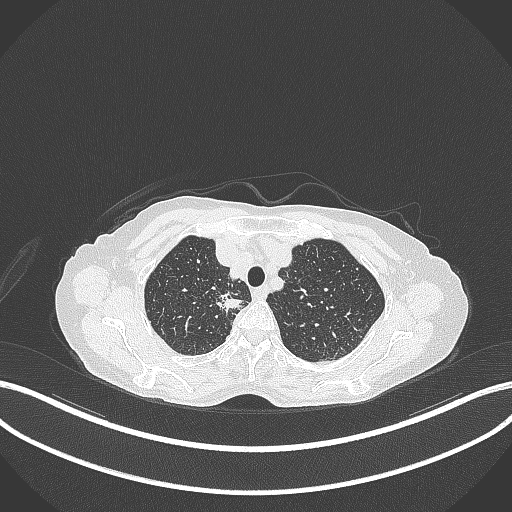
Chest CT, one axial slice; position 308 of 403 along the scan axis; reconstruction kernel B70f; 120 kVp; lung window (W 1500 / L -600 HU); 1 mm slice thickness; 512 × 512 image matrix. Female patient, age 75 years. From the clinical record (not read from this slice): clinical TNM (as recorded): T1c N1 M1.
Structures marked on this image (rectangle marked by the reading radiologist):
- lung tumour (recorded histology: adenocarcinoma): bounding box <214,293,249,315> (left, top, right, bottom; pixels)